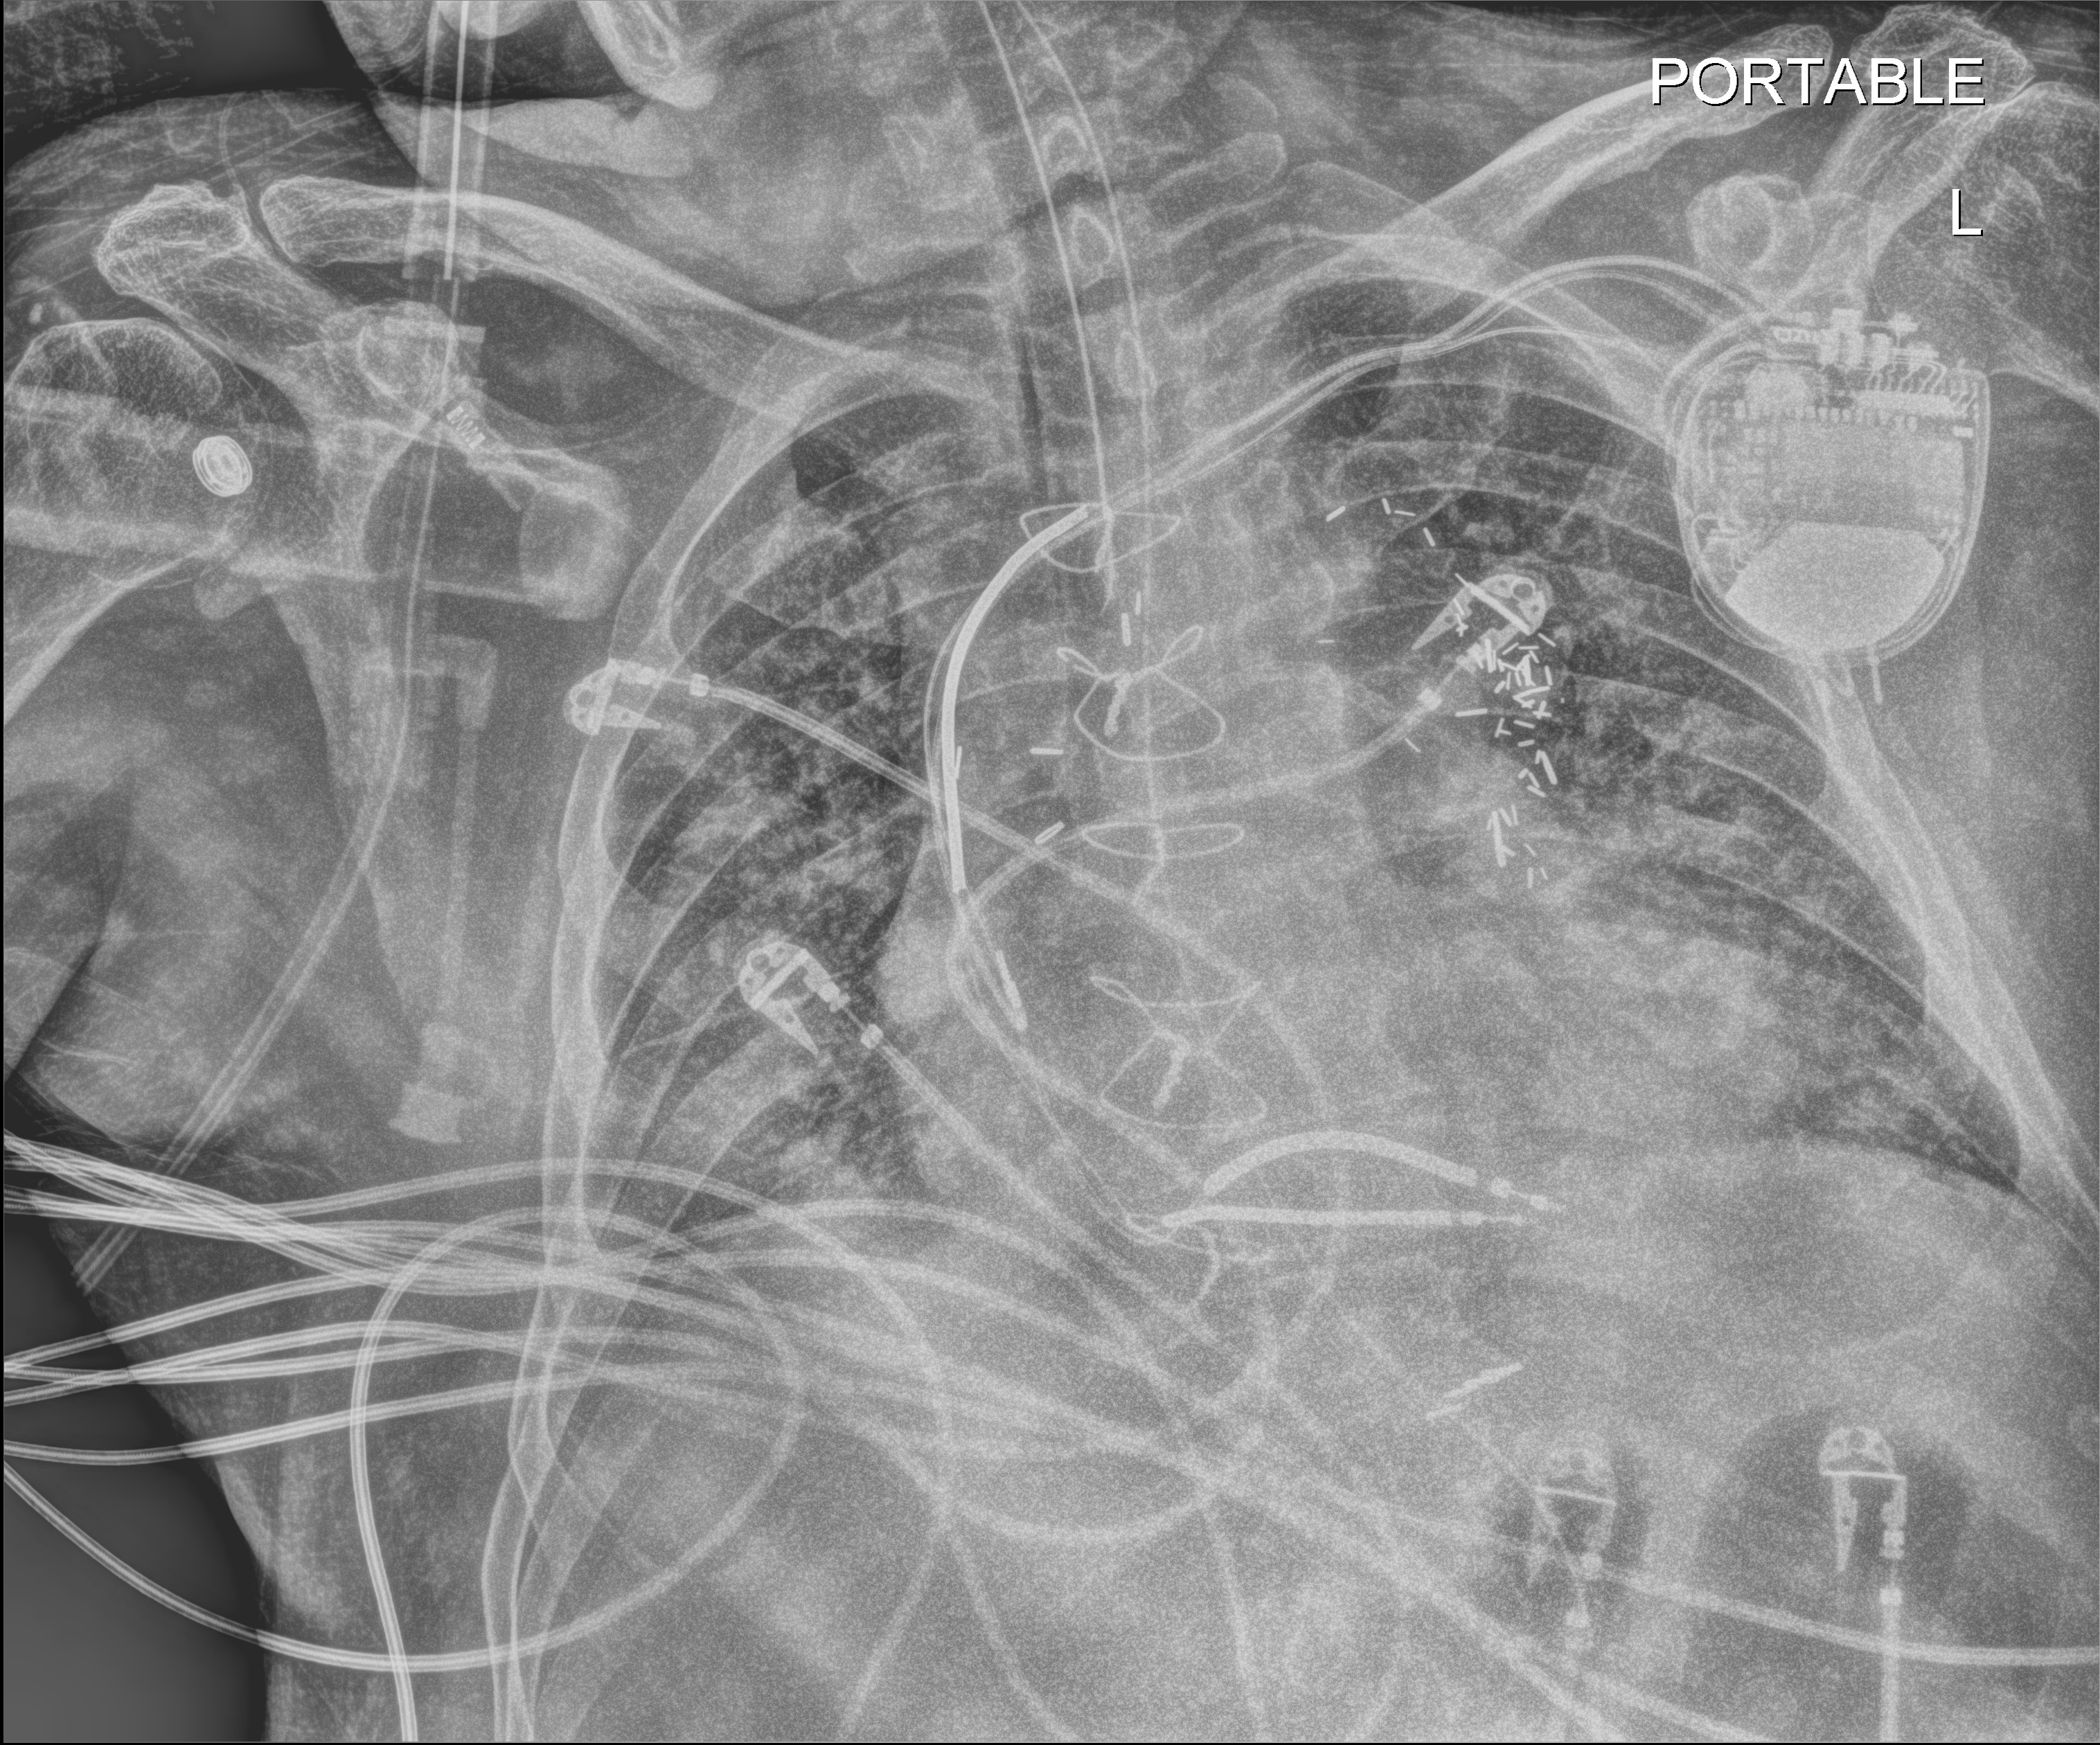
Bedside chest radiograph (digital radiography), anteroposterior (AP) projection. Patient hospitalised with COVID-19; male, aged 60–74 years.
From the hospital-stay record, not from the radiograph (when in the stay this image was taken is not recorded): COPD (admission record): no; admitted to intensive care during this hospital stay: yes; smoking status (admission record): never.